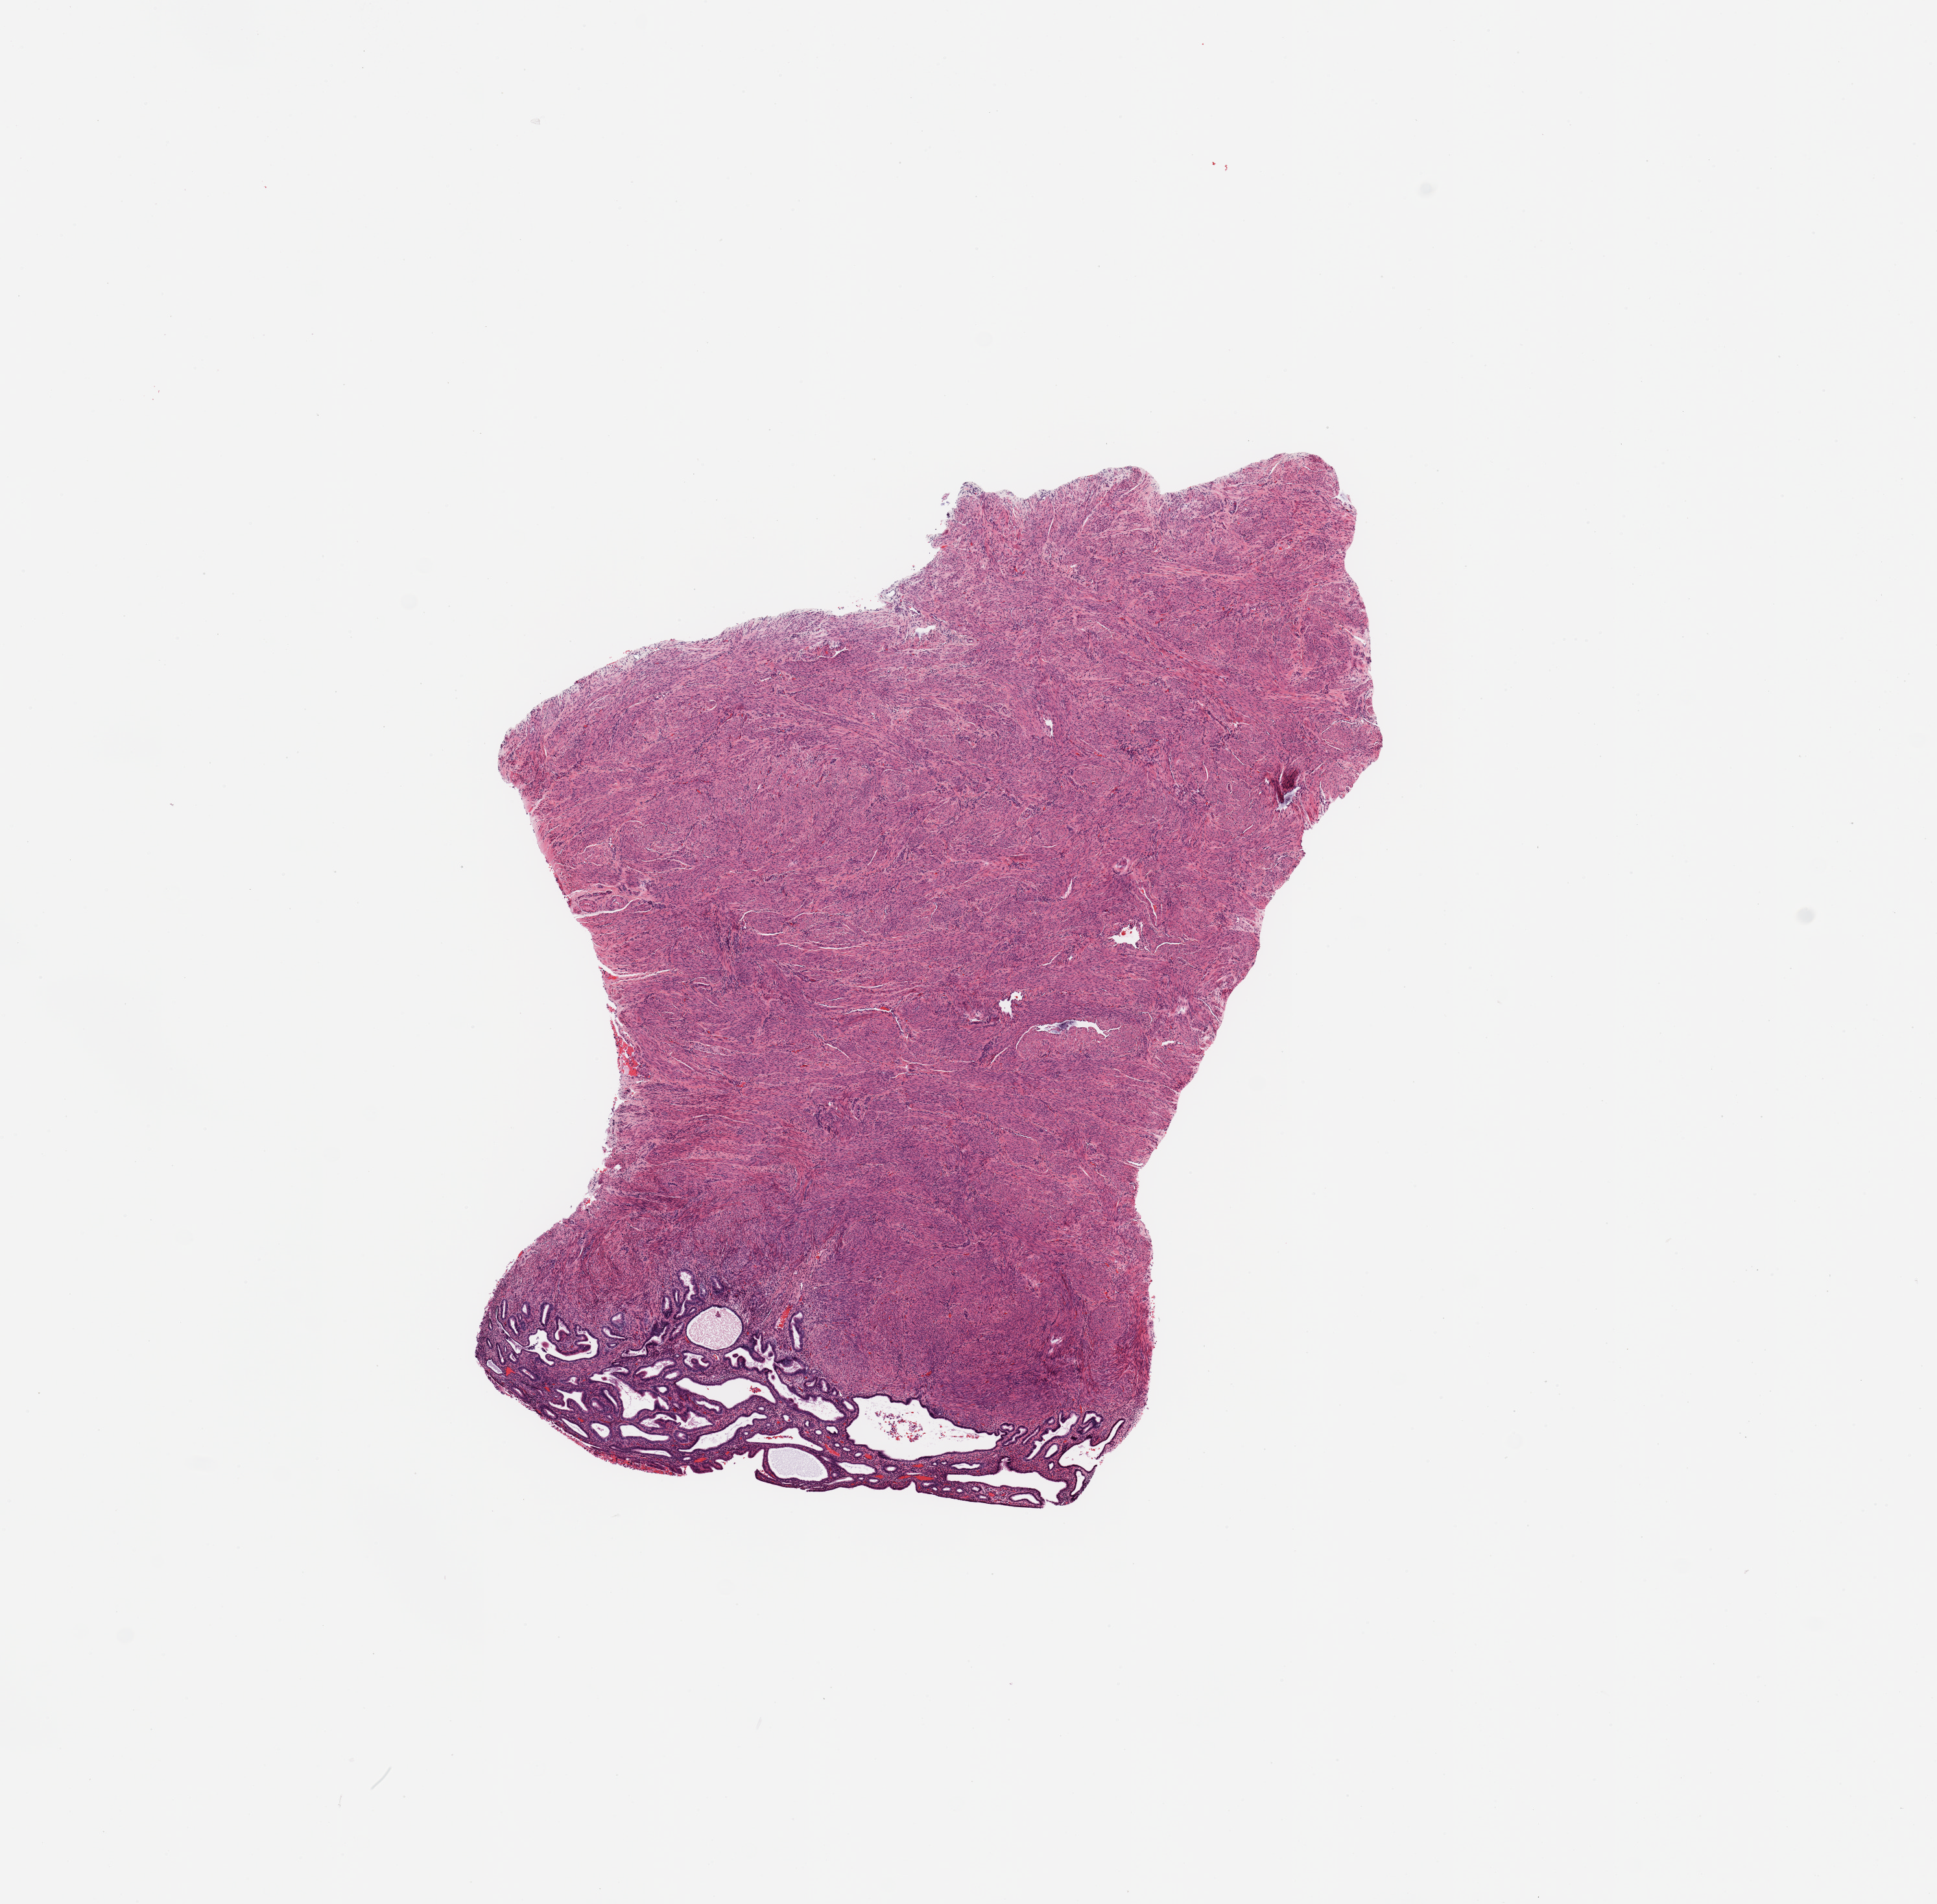
Digitized Hematoxylin and eosin (H&E) stained tissue section (whole slide), low-resolution overview of the scanned area, about 11.8 x 11.6 mm. Normal (non-tumour) tissue sample, sampled site: uterus. Patient: female, age 74 years.
- this section: normal (non-tumour) tissue from the same patient
- patient diagnosis: Endometrioid adenocarcinoma, NOS